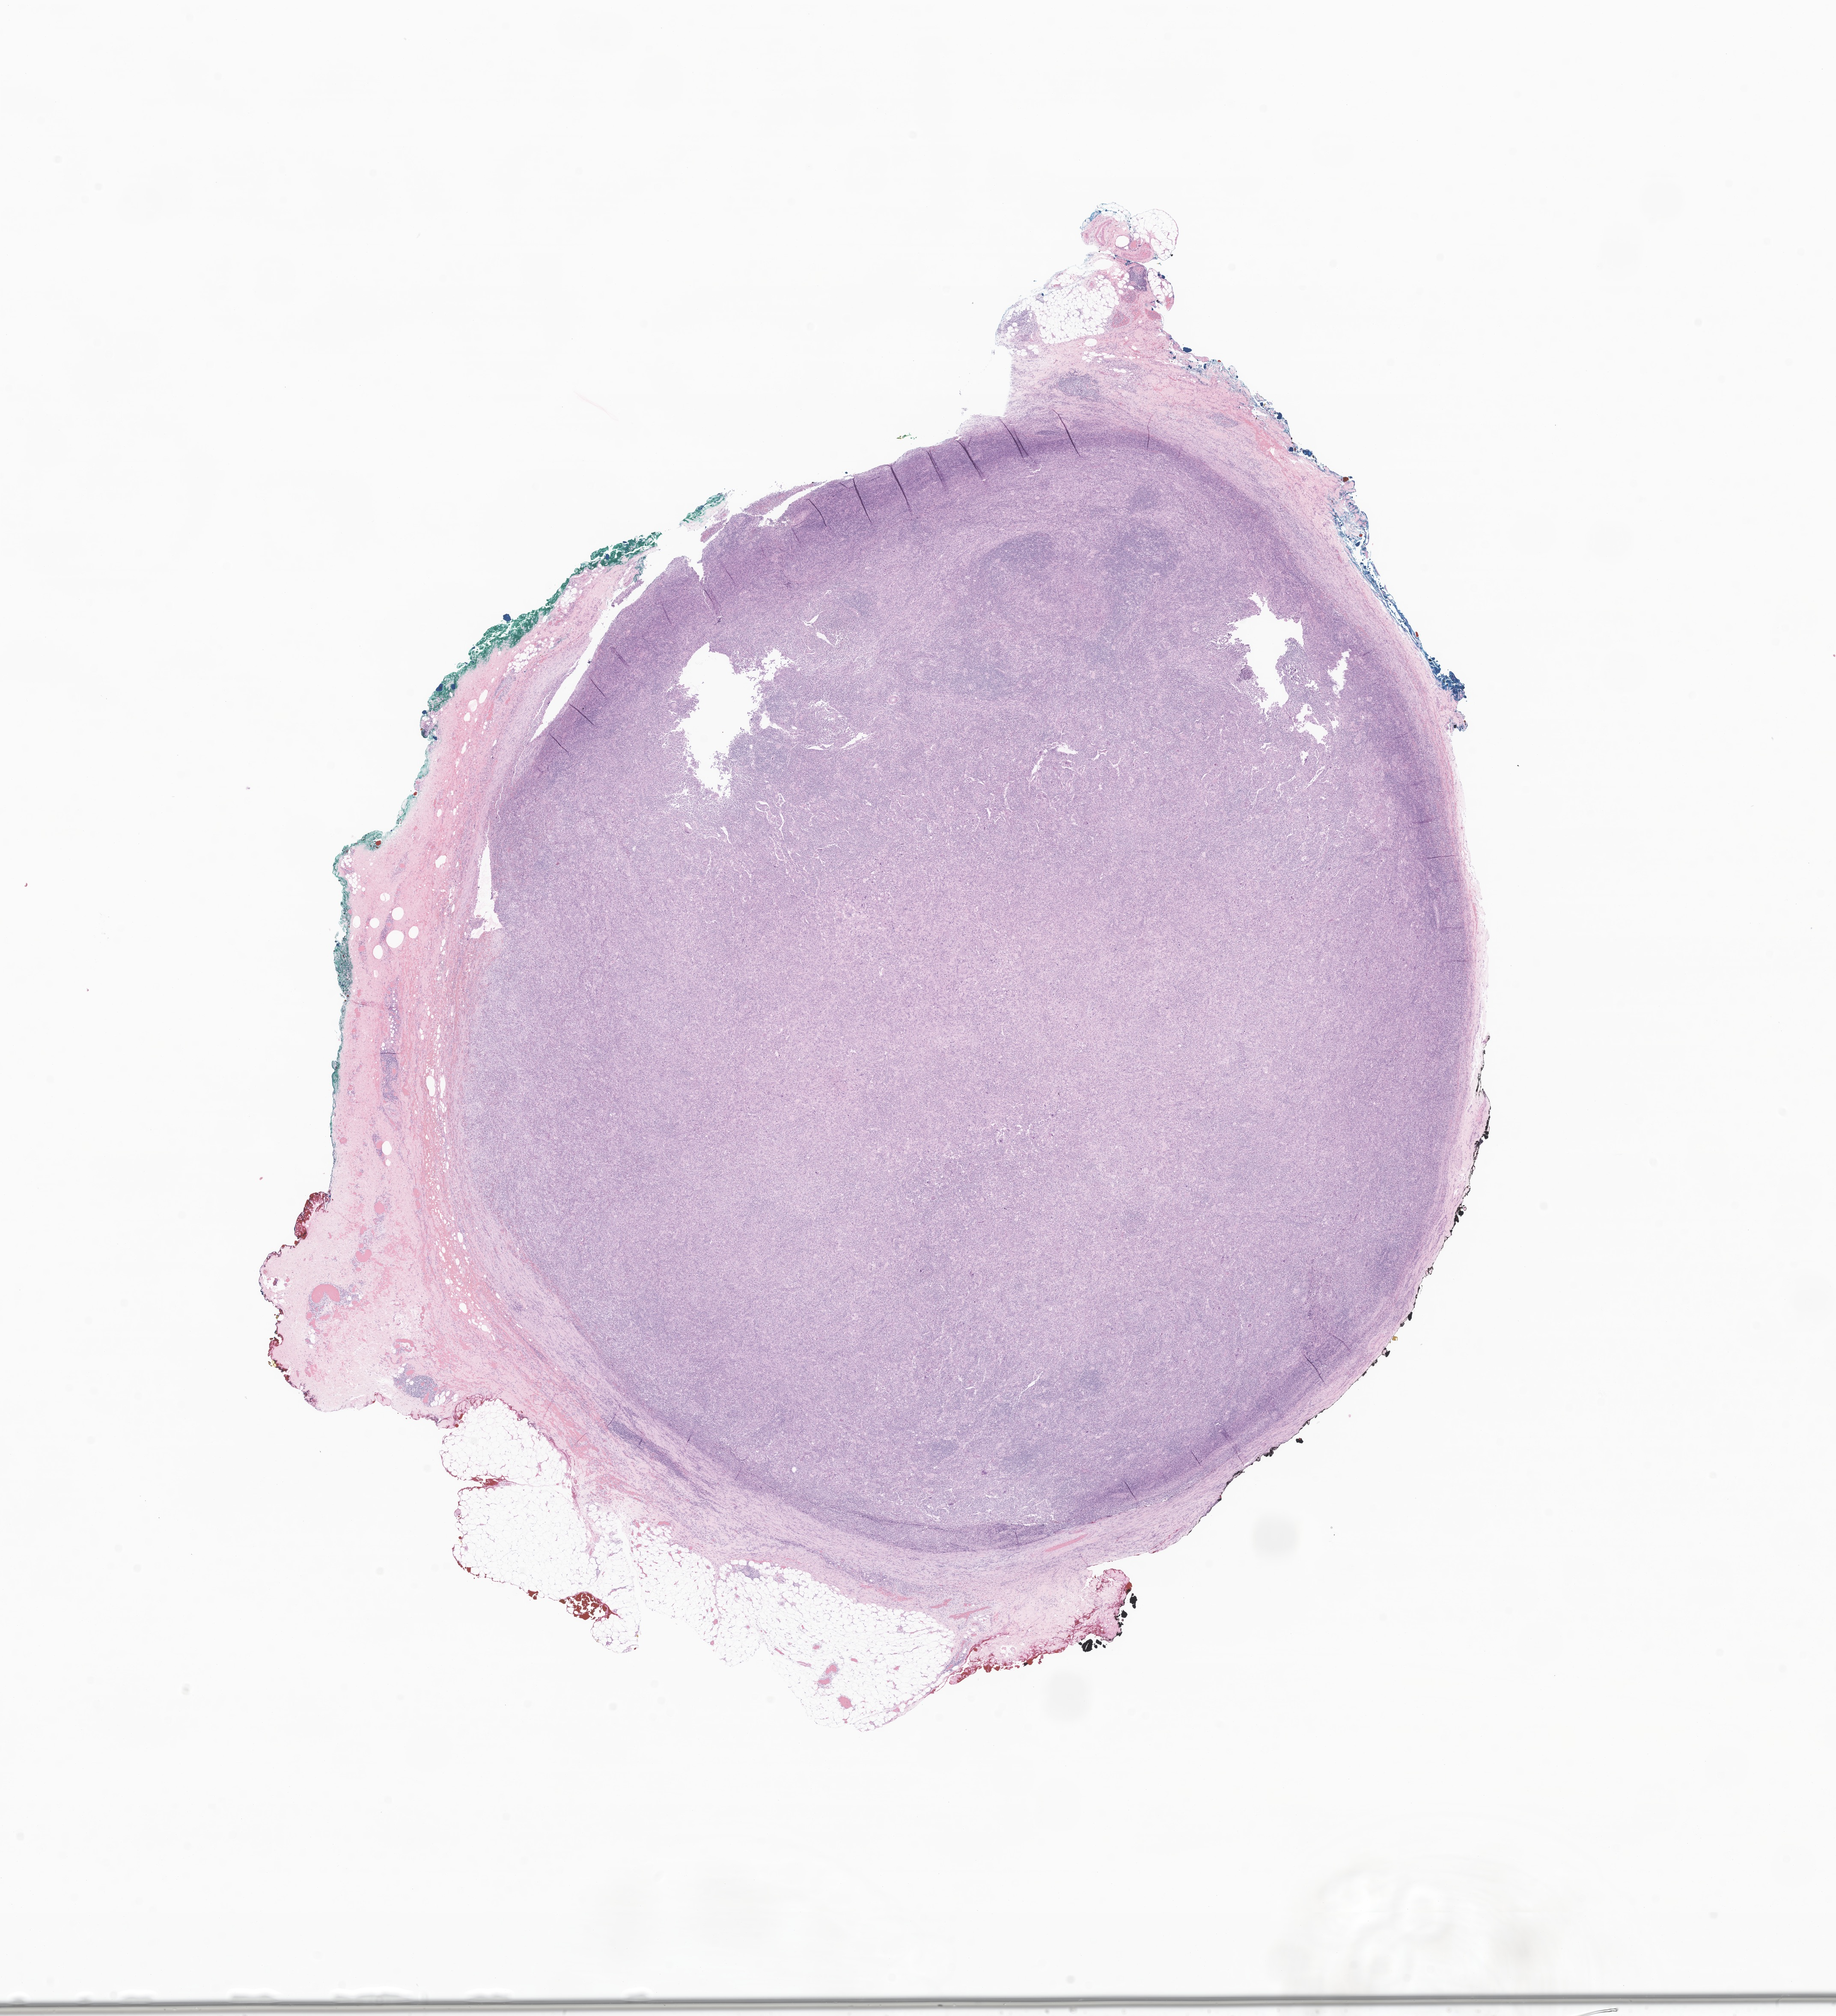
Hematoxylin and eosin (H&E) whole-slide image of tumor tissue from the soft tissue of abdomen, whole scanned area (about 18.1 x 19.9 mm) shown as a low-resolution overview; formalin-fixed, paraffin-embedded (FFPE) tissue. Patient female; age 216 months (18 years).
Recorded diagnosis: Undifferentiated sarcoma. Tissue or organ of origin (case record): connective, subcutaneous and other soft tissues of abdomen.